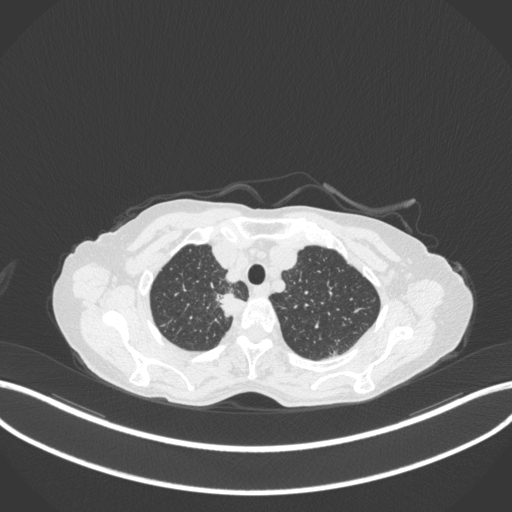
Chest CT, one axial slice; position 316 of 363 along the scan axis; reconstruction kernel B31f; 120 kVp; lung window (W 1500 / L -600 HU); 512 × 512 image matrix, field of view 400 × 400 mm. Patient: female, 75 years. From the clinical record (not read from this slice): clinical TNM (as recorded): T1c N1 M1.
Structures marked on this image (rectangle marked by the reading radiologist):
- lung tumour (recorded histology: adenocarcinoma): bounding box <214,288,250,323> (left, top, right, bottom; pixels)